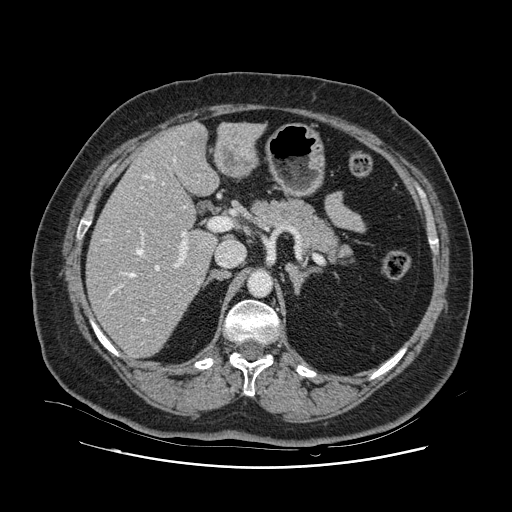
Contrast-enhanced abdominal CT, one axial slice; position 62 of 132 along the scan axis; intravenous contrast given; soft-tissue window (W 400 / L 40 HU); 512 × 512 image matrix, field of view 391 × 391 mm. Female patient, age 73 years. Case-level facts recorded for this patient, not image findings: diagnosis: colorectal cancer liver metastases, imaged before liver resection; multiple liver metastases: no; largest metastasis: 7 cm; disease in both lobes: no.
Structures marked on this image (manually delineated by an expert):
- hepatic veins: bounding box (x1, y1, x2, y2) in pixels: (105, 159, 199, 321)
- liver: (88, 124, 259, 357)
- planned liver remnant (the part of the liver to remain after resection): (88, 150, 216, 357)
- portal vein (with intrahepatic branches): (128, 218, 226, 311)
- liver metastasis: (219, 148, 253, 172)